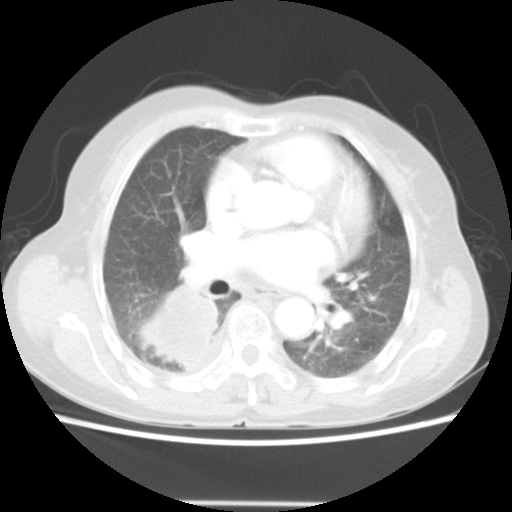
Chest CT, one axial slice; position 27 of 52 along the scan axis; reconstruction kernel STANDARD; 140 kVp; lung window (W 1500 / L -600 HU); 512 × 512 image matrix. Patient: female, 67 years. Case-level facts recorded for this patient, not image findings: clinical TNM (as recorded): T3 N1 M1.
Structures marked on this image (bounding box drawn by a radiologist):
- lung tumour (recorded histology: adenocarcinoma): box from (x=134, y=281) to (x=224, y=371) px